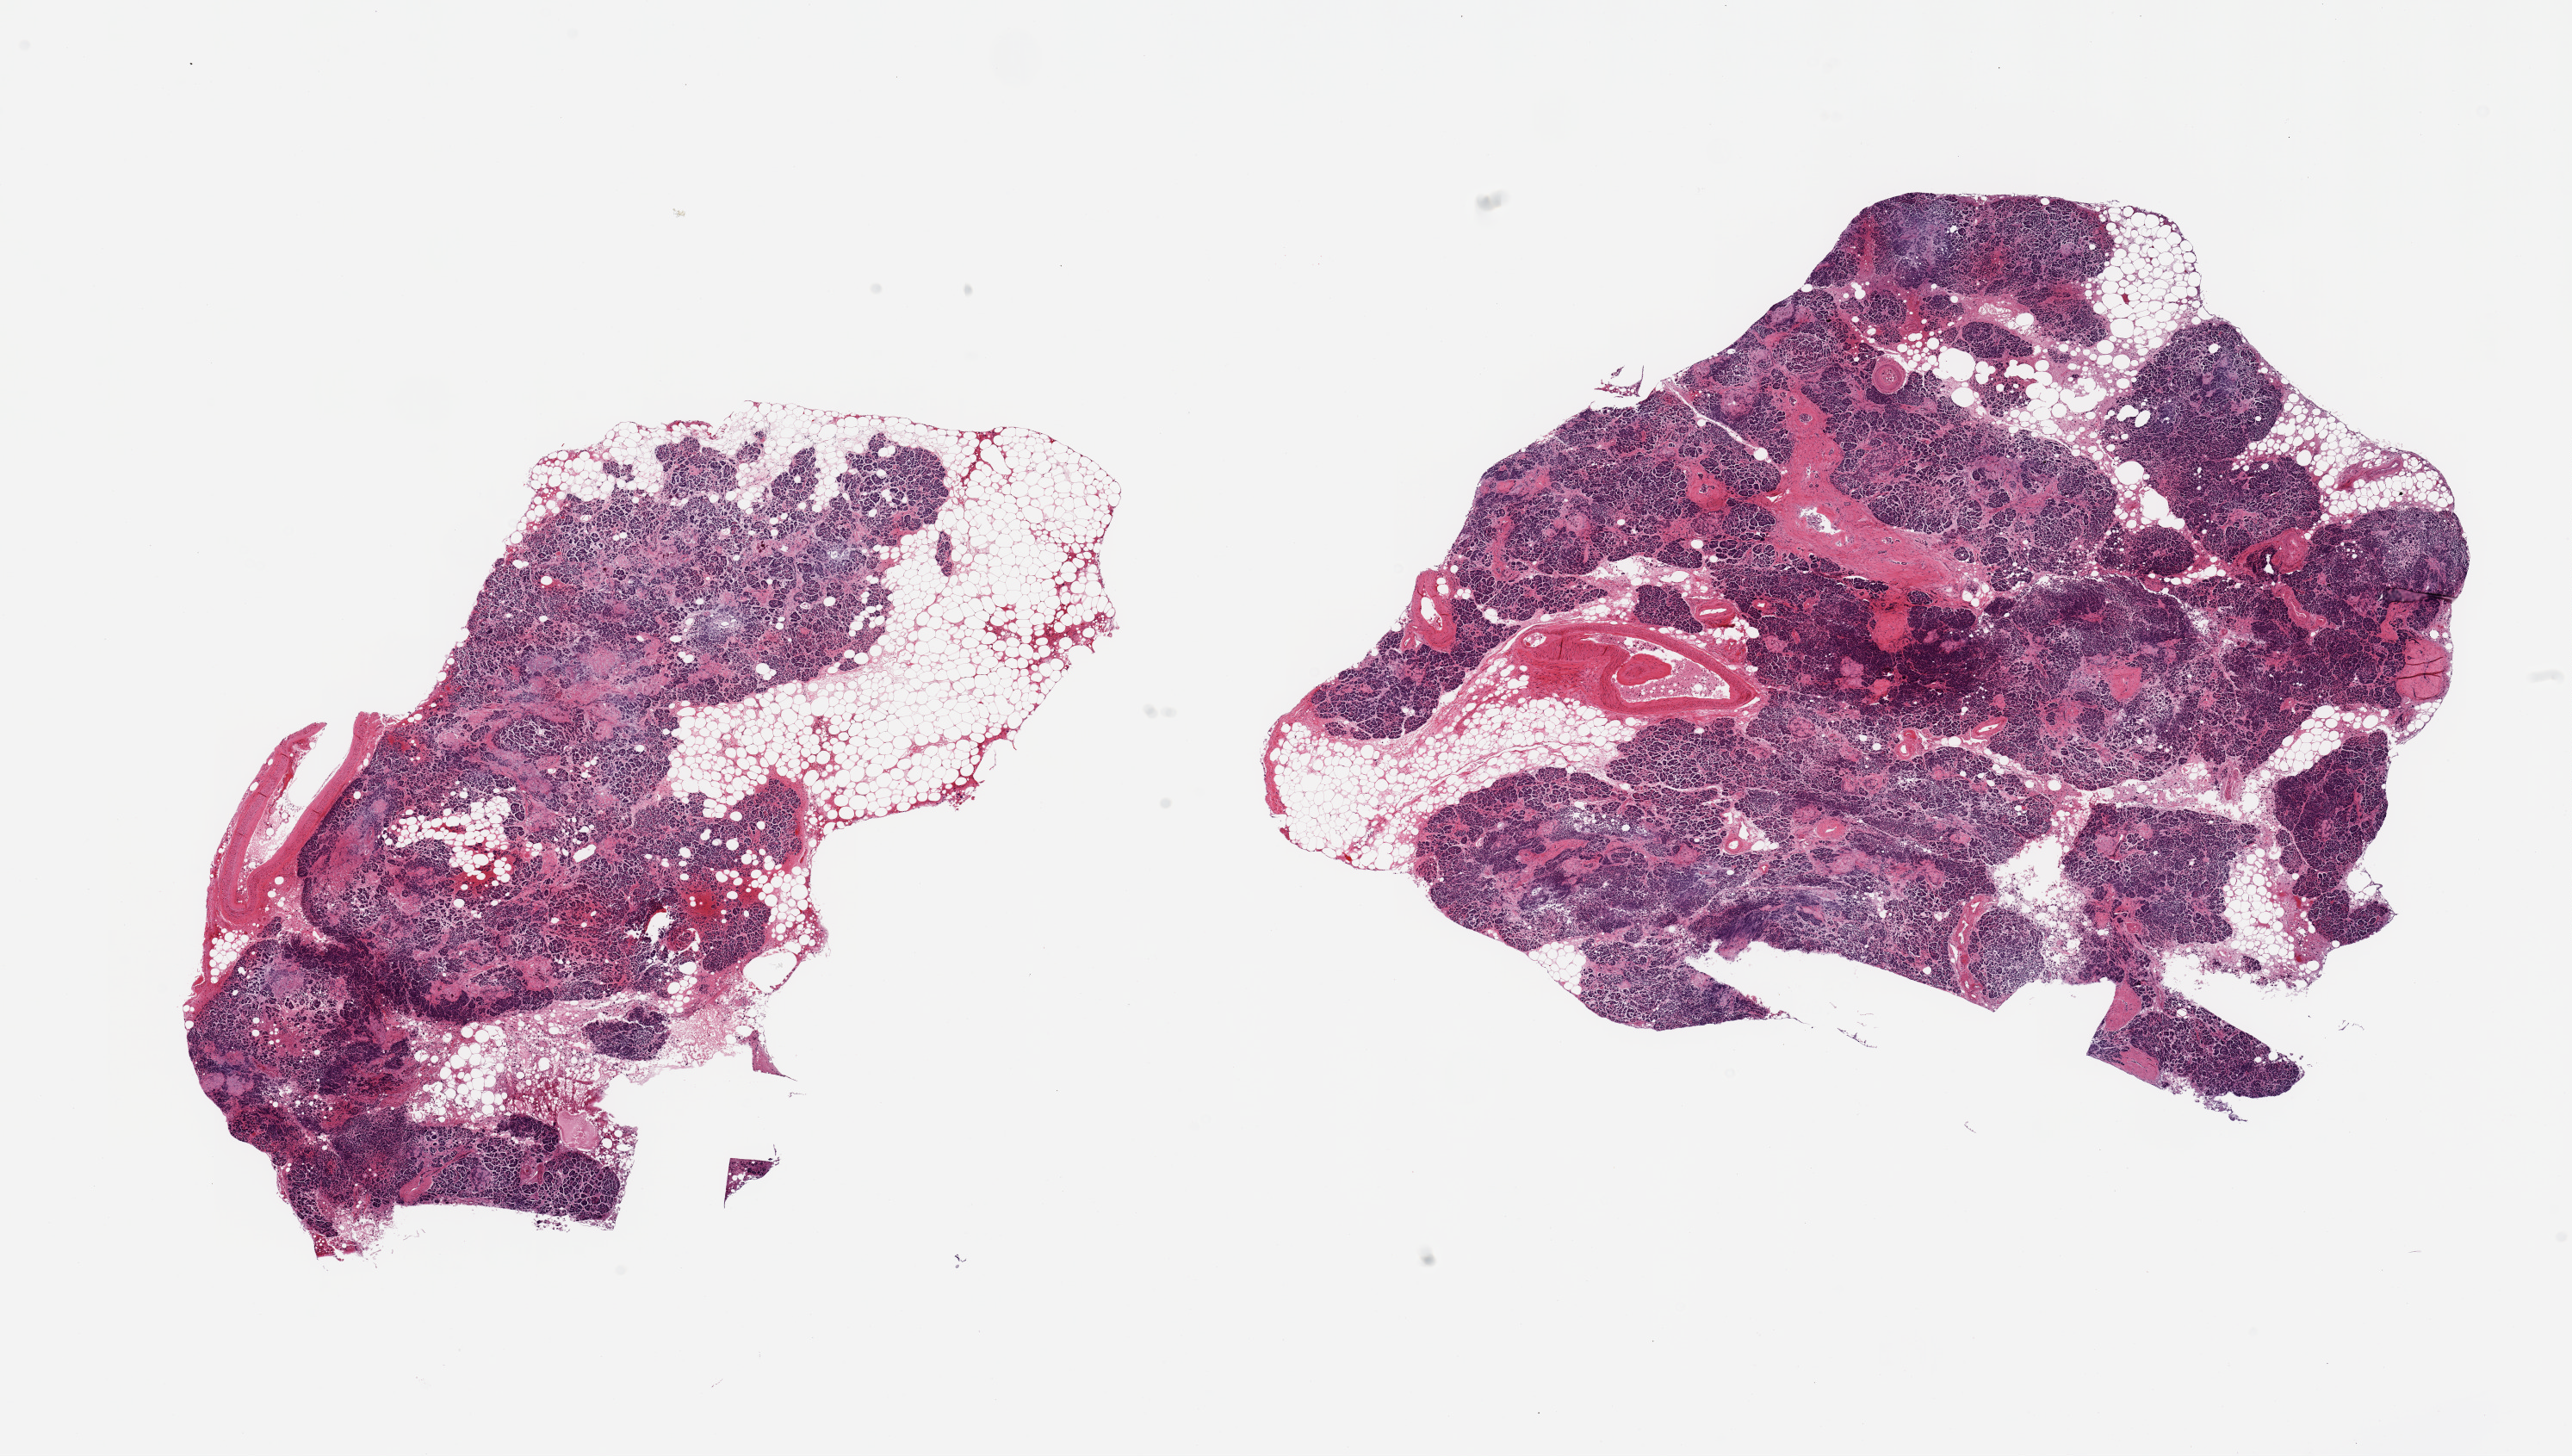
Digitized hematoxylin and eosin (H&E)-stained section, whole scanned area (about 23.6 x 13.4 mm, from a 20x scan) shown as a low-resolution overview. PAXgene-fixed, paraffin-embedded tissue. Target tissue: pancreas. Tissue donor sample. Donor sex: male.
- review note (as recorded): 2 pieces; 30% external & internal adipose content; moderate (up to 20%) interstitial fibrosis including islets